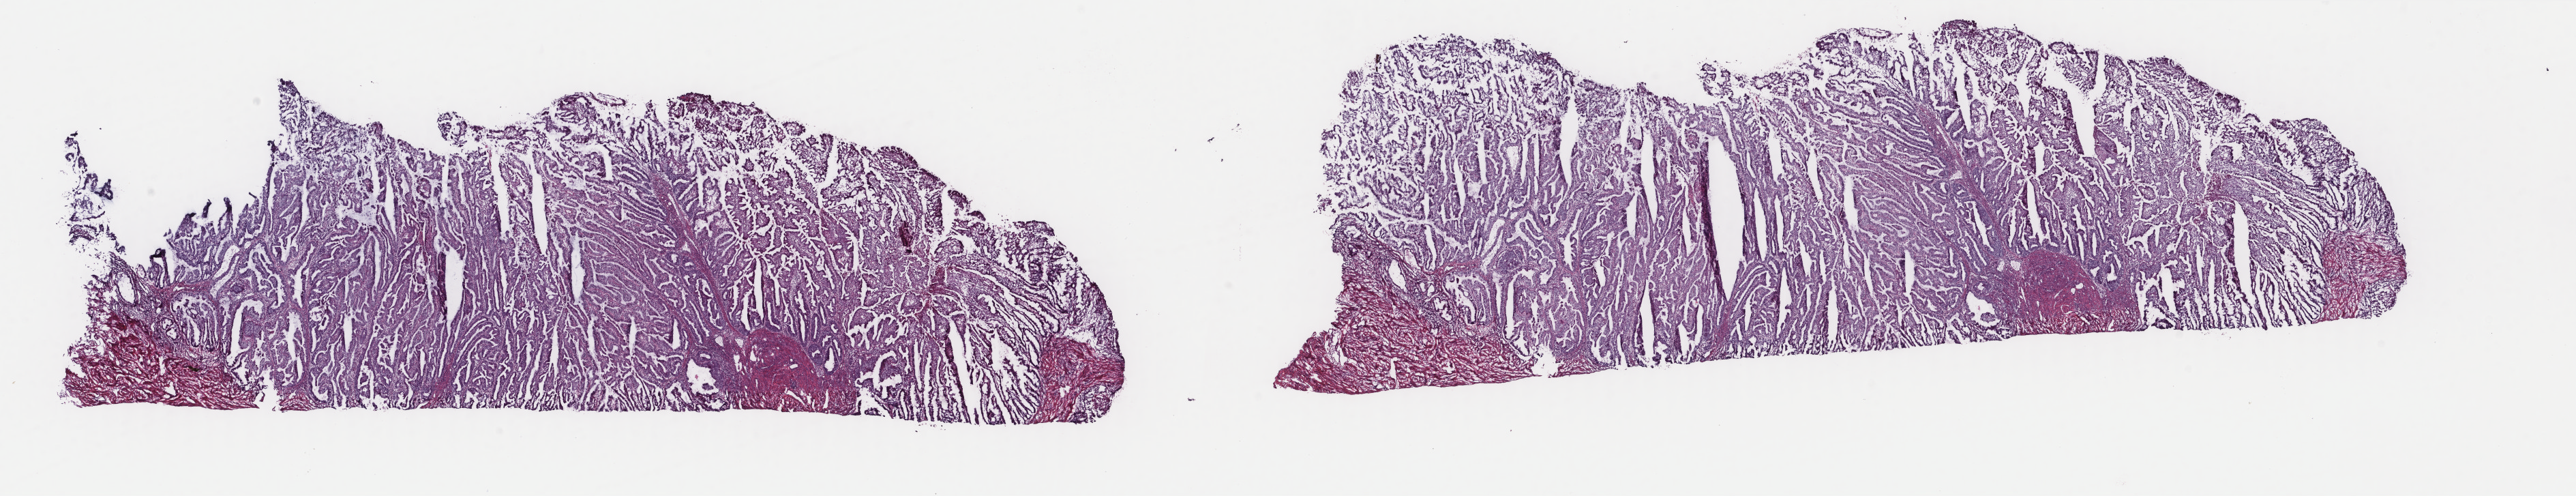
H&E-stained whole-slide image — low-resolution overview of the scanned area, about 30.0 x 5.8 mm (from a 40x scan); frozen section from the top of the tissue portion; uterus, primary tumour sample. Female, age 58 years at initial diagnosis. Histologic grade: G1 (well differentiated). Pathologist review of this section (percent, as recorded): tumour cells 95%, tumour nuclei 80%, normal cells 5%, stromal cells 0%, necrosis 0%. Inflammatory infiltration, as recorded: lymphocyte infiltration 0%, monocyte infiltration 0%, neutrophil infiltration 0%.
Histologic diagnosis: Endometrioid adenocarcinoma, NOS. FIGO stage: IIIC.